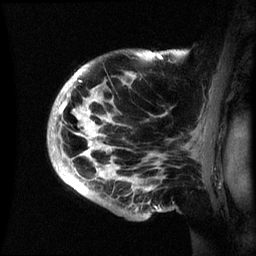
Breast MRI (dynamic contrast-enhanced), one sagittal slice; slice 46 of 60 in the series (ordered by position); dynamic contrast-enhanced series, image 2 of 3 at this slice position (ordered by acquisition); 1.5 T; TE 4.2 ms, TR 8.4 ms; 2.4 mm slice thickness; 256 × 256 image matrix, field of view 230 × 230 mm. Female patient, age 48 years.
Annotated regions visible in this slice (semi-automatic segmentation, software-assisted and operator-edited):
- analysis volume of interest (the breast-tissue region the enhancement analysis was run in; not a lesion): box from (x=48, y=50) to (x=195, y=220) px
- tumour enhancement mask (voxels above the 70 % enhancement threshold inside the analysis volume of interest): (x=60, y=79)–(x=109, y=175)